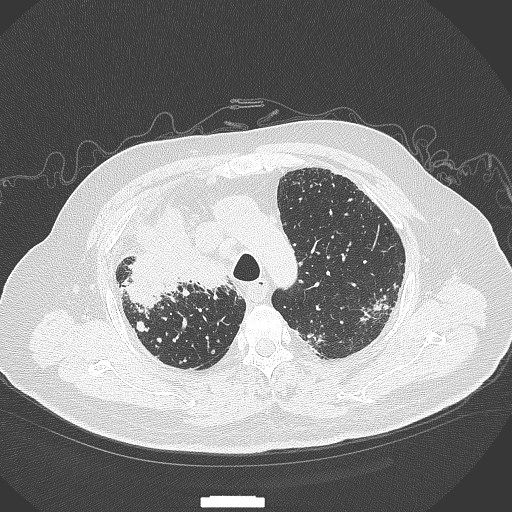
Chest CT, one axial slice. Position 276 of 384 along the scan axis. Reconstruction kernel B70f. 120 kVp. Lung window (W 1500 / L -600 HU). 1 mm slice thickness. 512 × 512 image matrix, field of view 400 × 400 mm. Male patient, age 69 years. Case-level facts recorded for this patient, not image findings: clinical TNM (as recorded): T4 N3 M1.
Structures marked on this image (rectangle marked by the reading radiologist):
- lung tumour (recorded histology: adenocarcinoma): bounding box (x1, y1, x2, y2) in pixels: (126, 210, 233, 306)